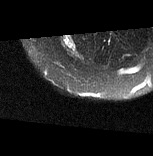
MRI of an extremity soft-tissue mass, one axial slice. Slice 12 of 77 in the series (ordered by position). T2-weighted fat-saturated. MR volume resampled by the dataset authors to the PET/CT grid (not the native acquisition matrix). 3.27 mm slice thickness. 153 × 156 image matrix, field of view 149 × 152 mm. Female patient. Case-level facts recorded for this patient, not image findings: histological type: synovial sarcoma; grade: intermediate; site of the primary tumour: right buttock.
Outlined on this slice (expert contour drawn on MRI and transferred to this co-registered scan by the dataset authors):
- gross tumour volume including surrounding oedema: box from (x=62, y=34) to (x=77, y=55) px